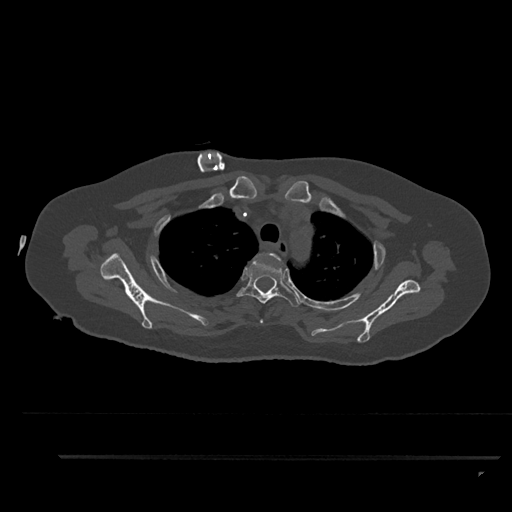
CT including the spine, one axial slice; position 691 of 797 along the scan axis; reconstruction kernel Br40s/3; 120 kVp; bone window (W 1800 / L 400 HU); 0.5 mm slice thickness; 512 × 512 image matrix, field of view 408 × 408 mm. Female patient, age 44 years. From the clinical record (not read from this slice): primary cancer: renal; vertebrae with lytic lesions (as recorded): L1.
Annotated regions visible in this slice (semi-automatic segmentation, software-assisted and operator-edited):
- T2 vertebra: bounding box (x1, y1, x2, y2) in pixels: (260, 253, 281, 324)
- T3 vertebra: (236, 256, 301, 307)